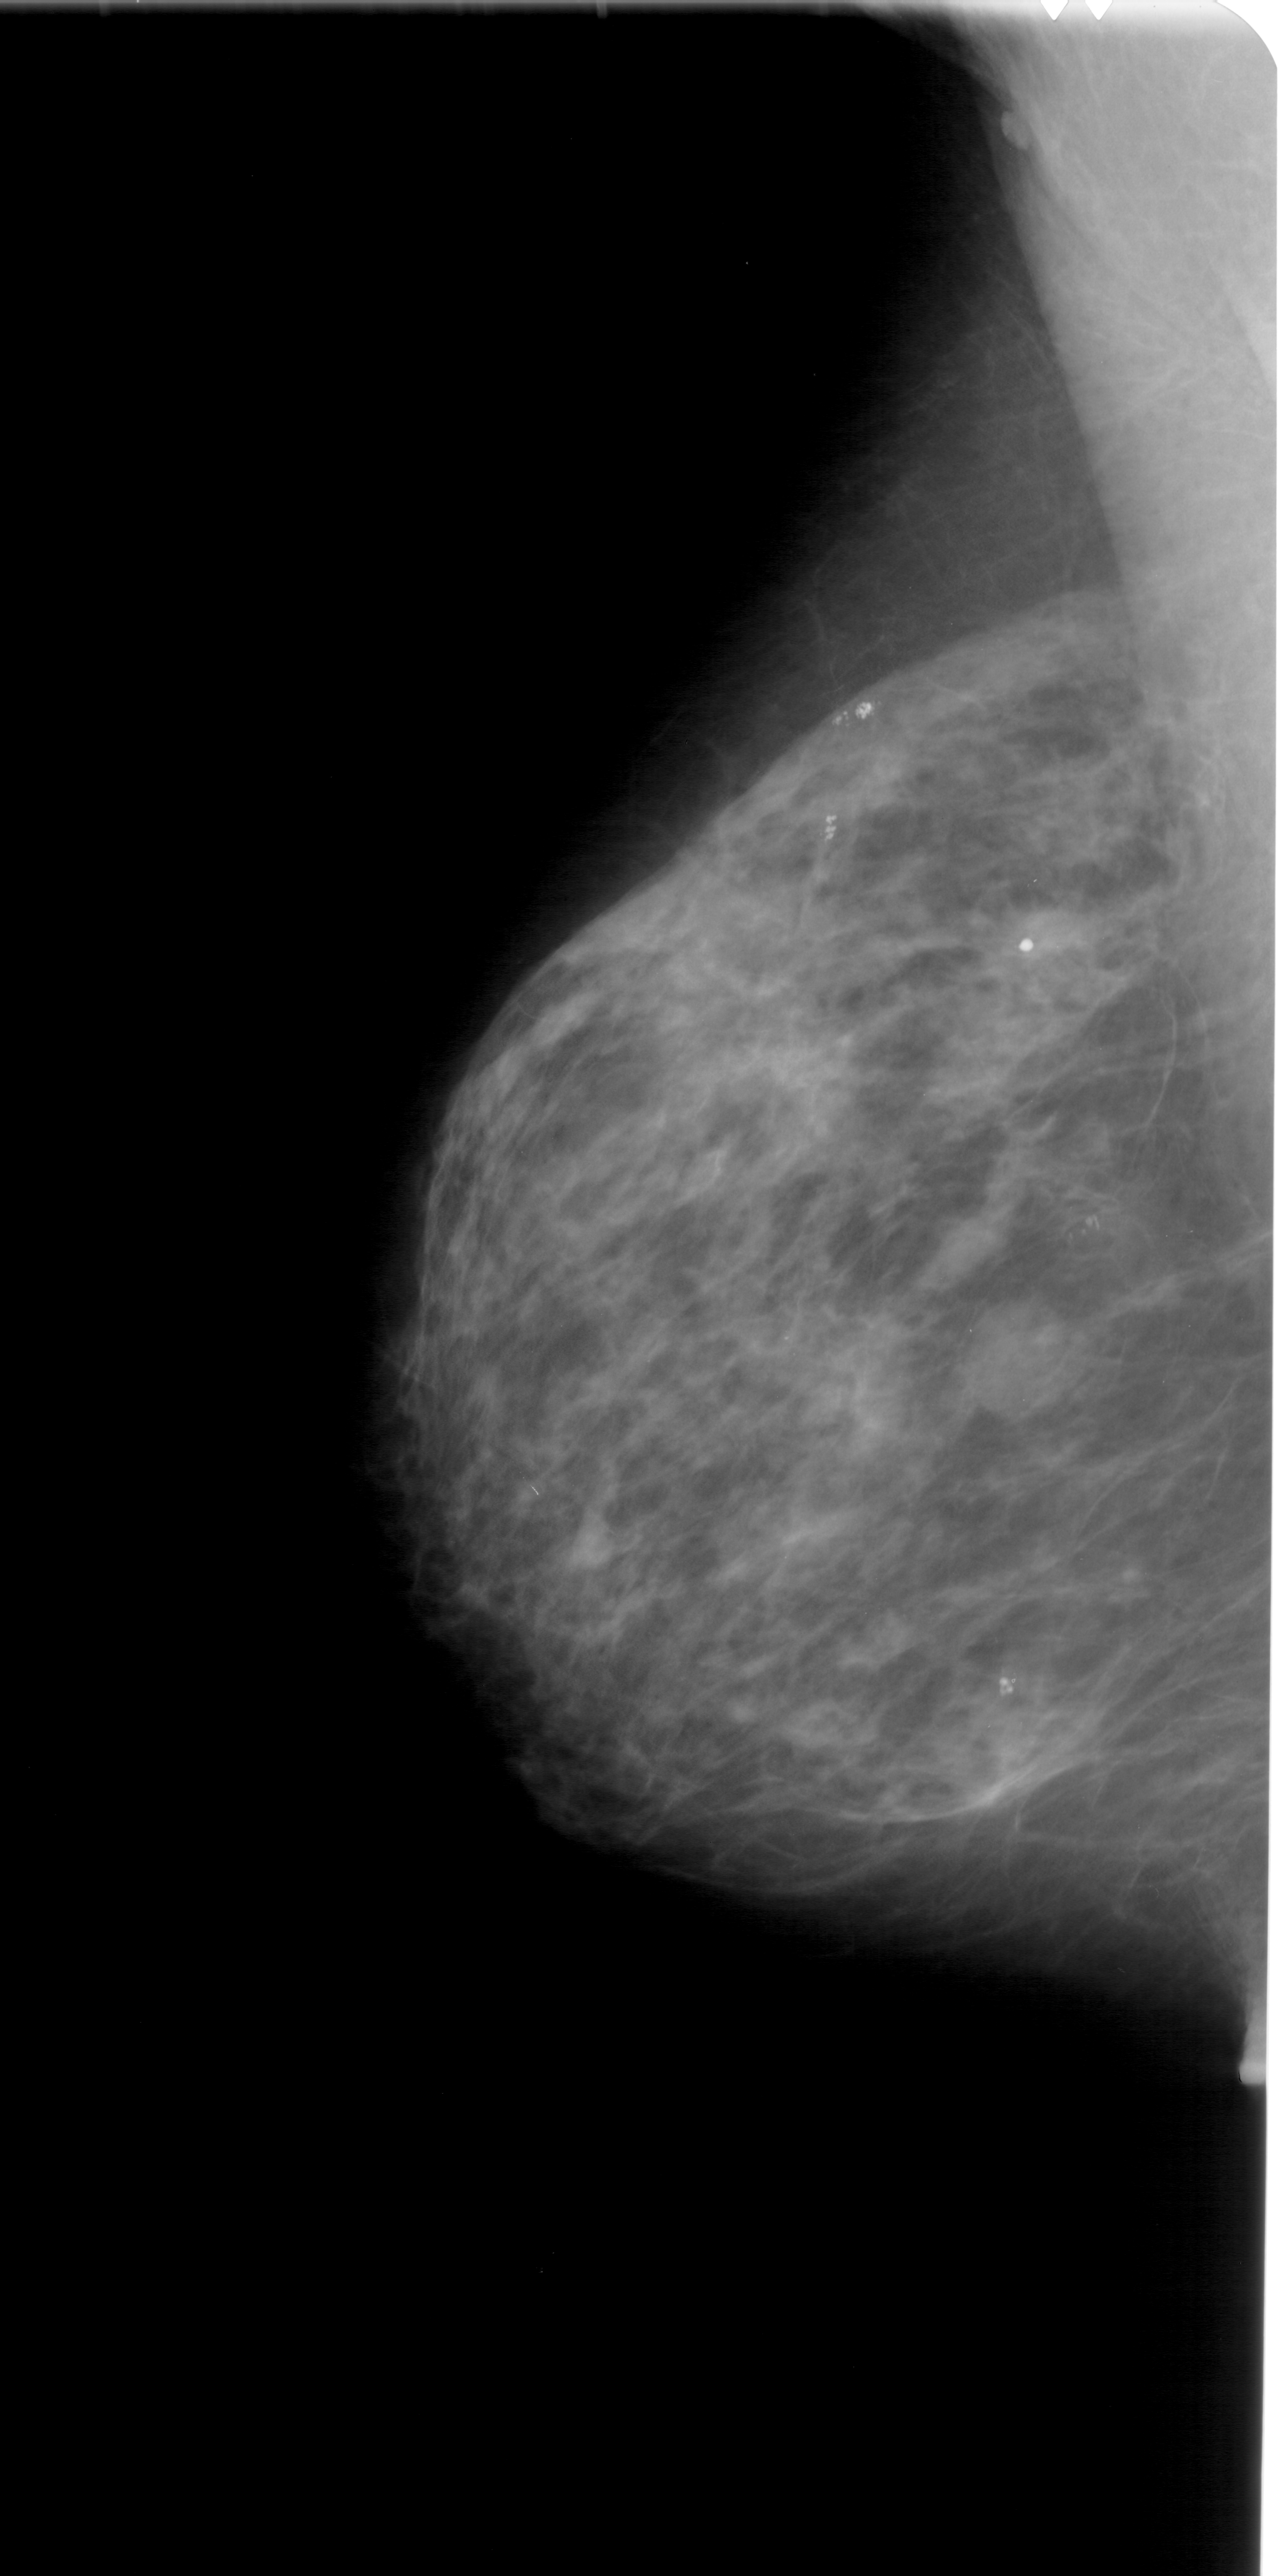
Digitized screen-film mammogram, left breast, MLO view, breast composition: heterogeneously dense (BI-RADS density category 3 of 4).
- Abnormality record for this image: mass, shape lobulated, margins ill defined; BI-RADS assessment category 4; pathology (as recorded): benign.